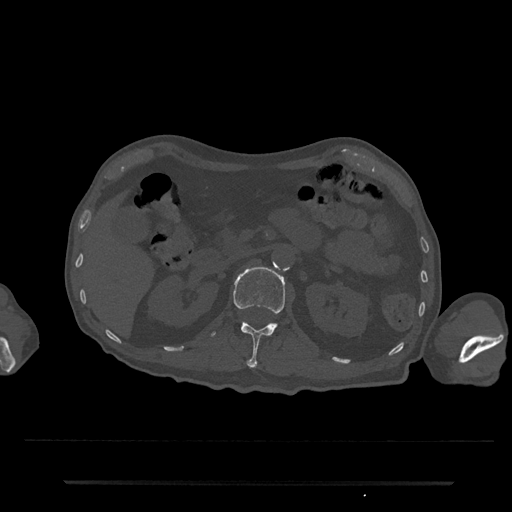
CT including the spine, one axial slice. Position 122 of 797 along the scan axis. Reconstruction kernel Br40s/3. 120 kVp. Bone window (W 1800 / L 400 HU). 512 × 512 image matrix. Patient: male, 74 years. Case-level facts recorded for this patient, not image findings: primary cancer: prostate.
Annotated regions visible in this slice (semi-automatically segmented with operator editing):
- L1 vertebra: bounding box [x1, y1, x2, y2] px = [210, 267, 285, 368]